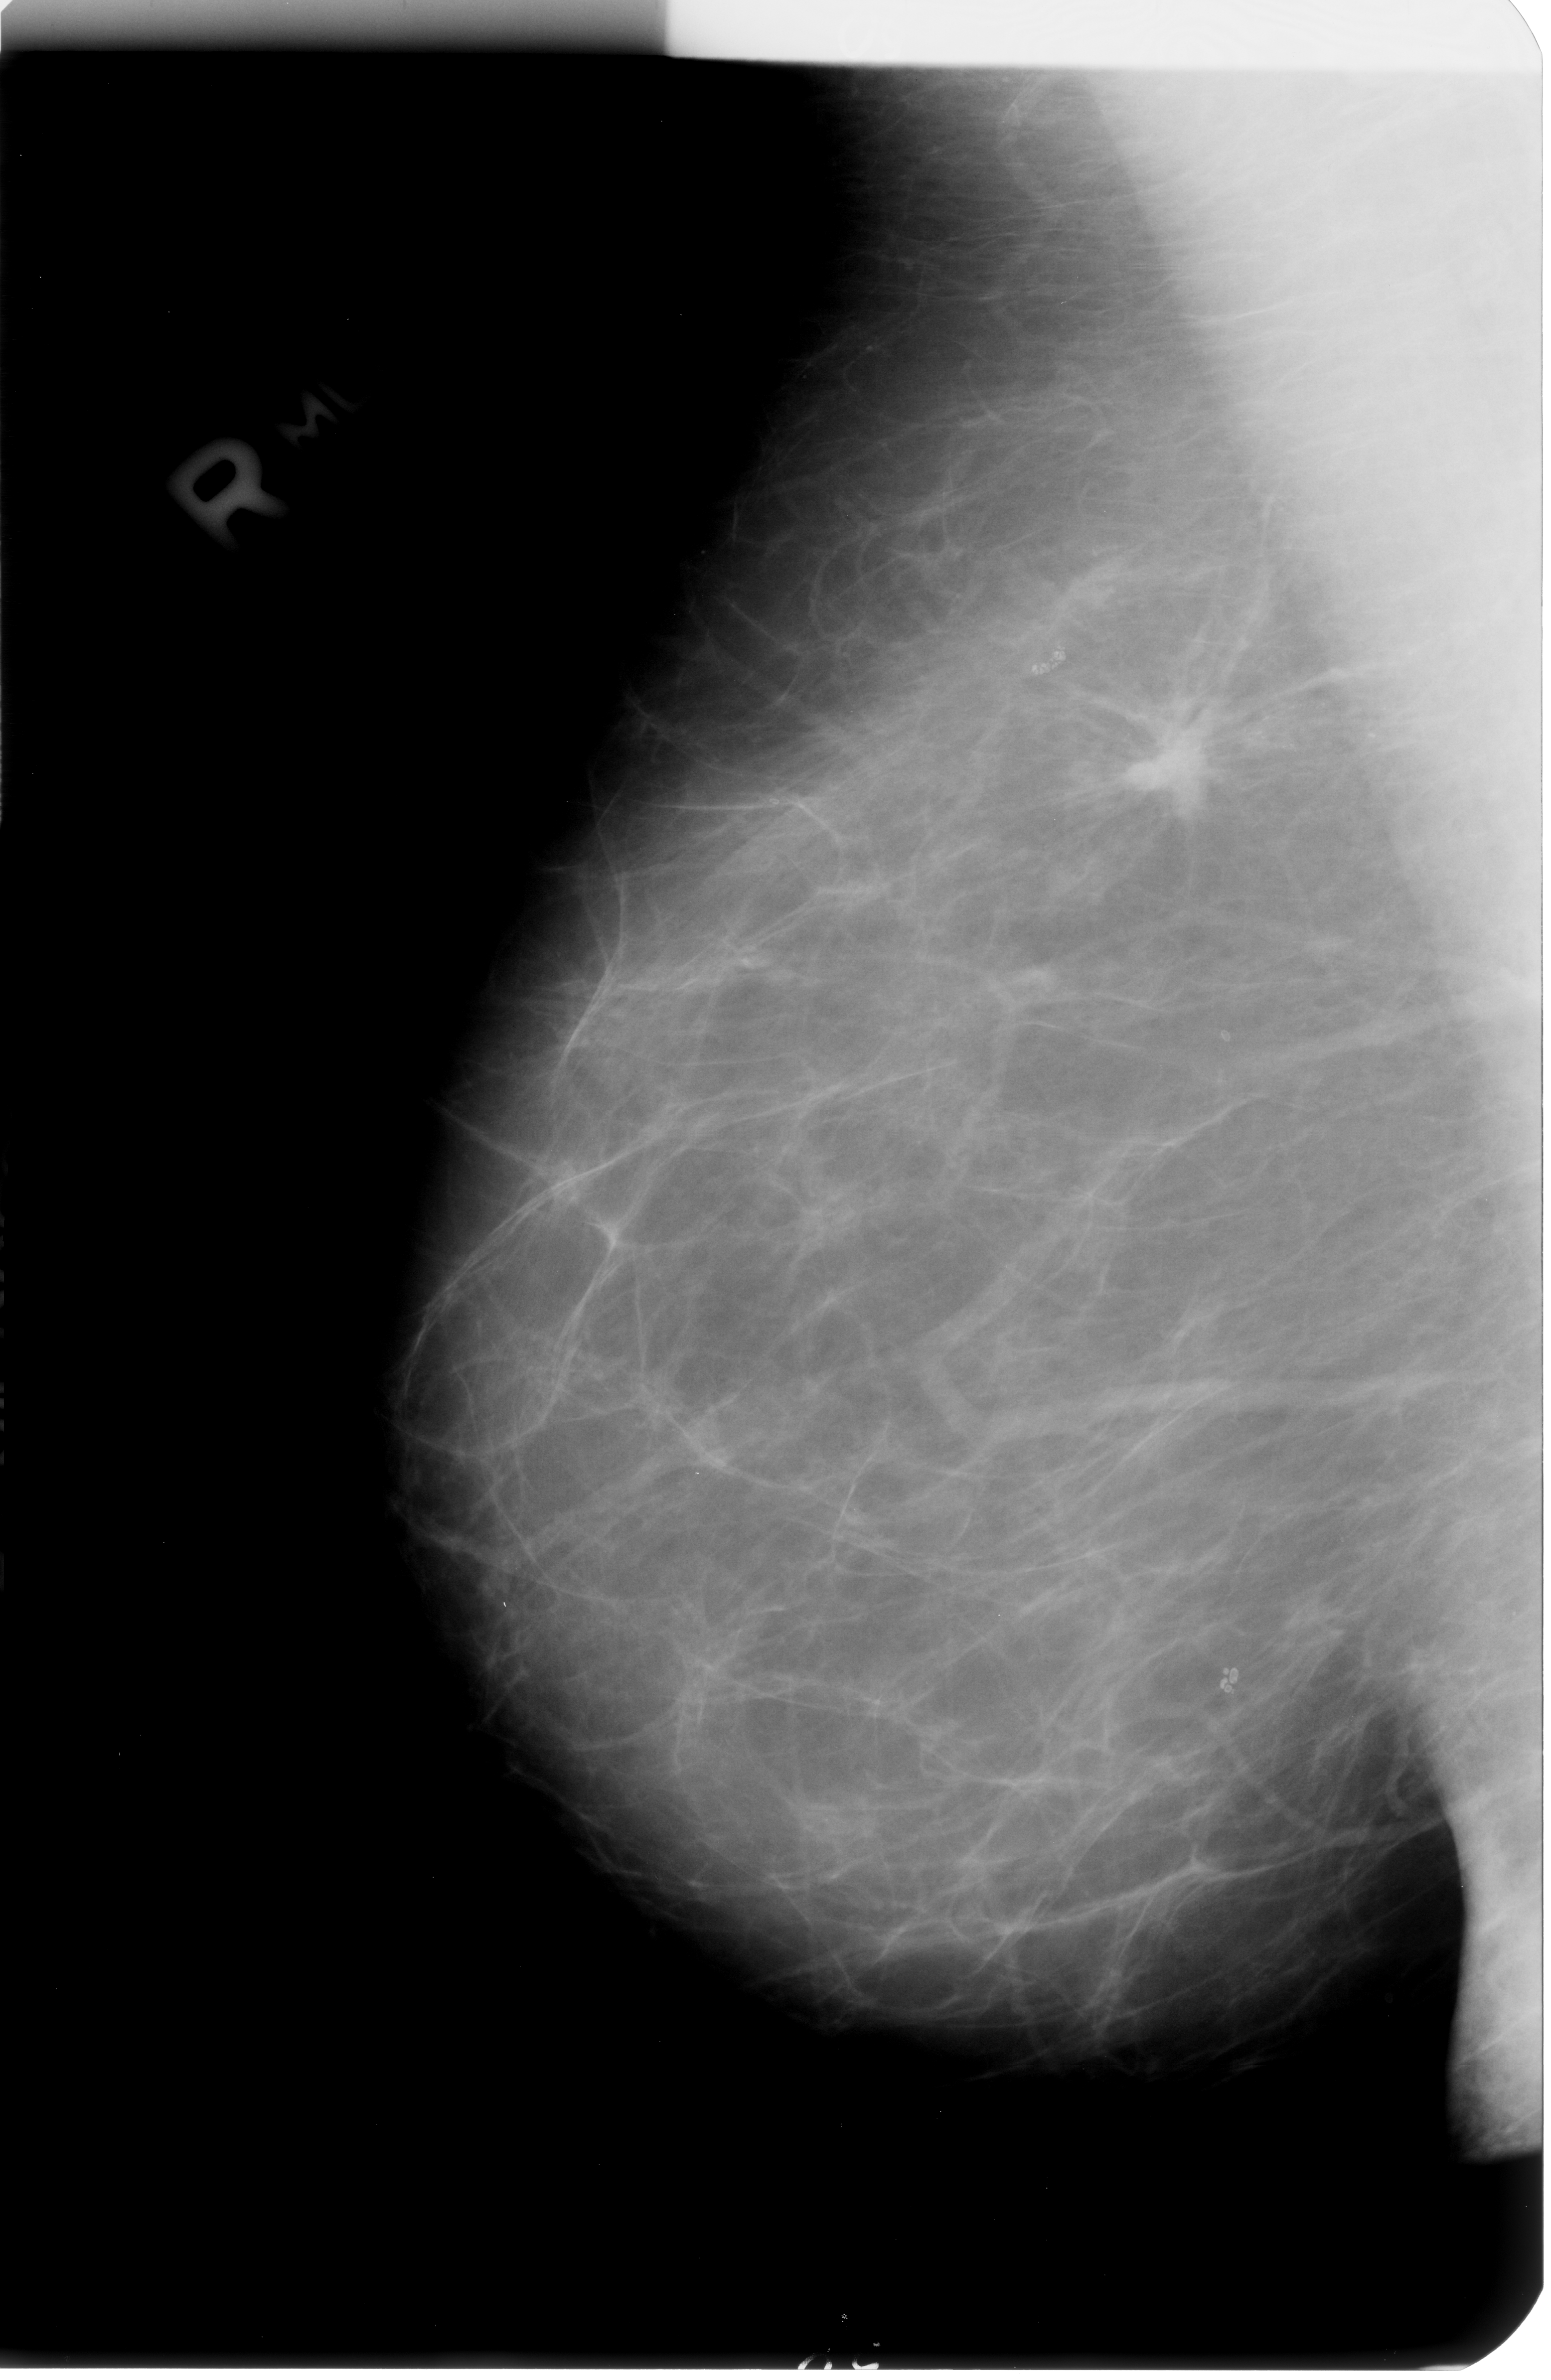
Digitized screen-film mammogram; right breast; mediolateral oblique (MLO) view; breast composition: almost entirely fatty (BI-RADS density category 1 of 4).
Marked findings (only marked abnormalities are described; nothing is implied about the rest of the image): Finding 1 of 3: calcifications, morphology fine linear branching, distribution clustered / linear; BI-RADS assessment category 5; subtlety rating 4 on a 1 (subtle) to 5 (obvious) scale; pathology result (as recorded, not read from the image): malignant. Finding 2 of 3: calcifications, morphology fine linear branching, distribution clustered / linear; BI-RADS assessment category 5; subtlety rating 4 on a 1 (subtle) to 5 (obvious) scale; pathology result (as recorded, not read from the image): malignant. Finding 3 of 3: calcifications, morphology fine linear branching, distribution clustered / linear; BI-RADS assessment category 5; pathology result (as recorded, not read from the image): malignant.